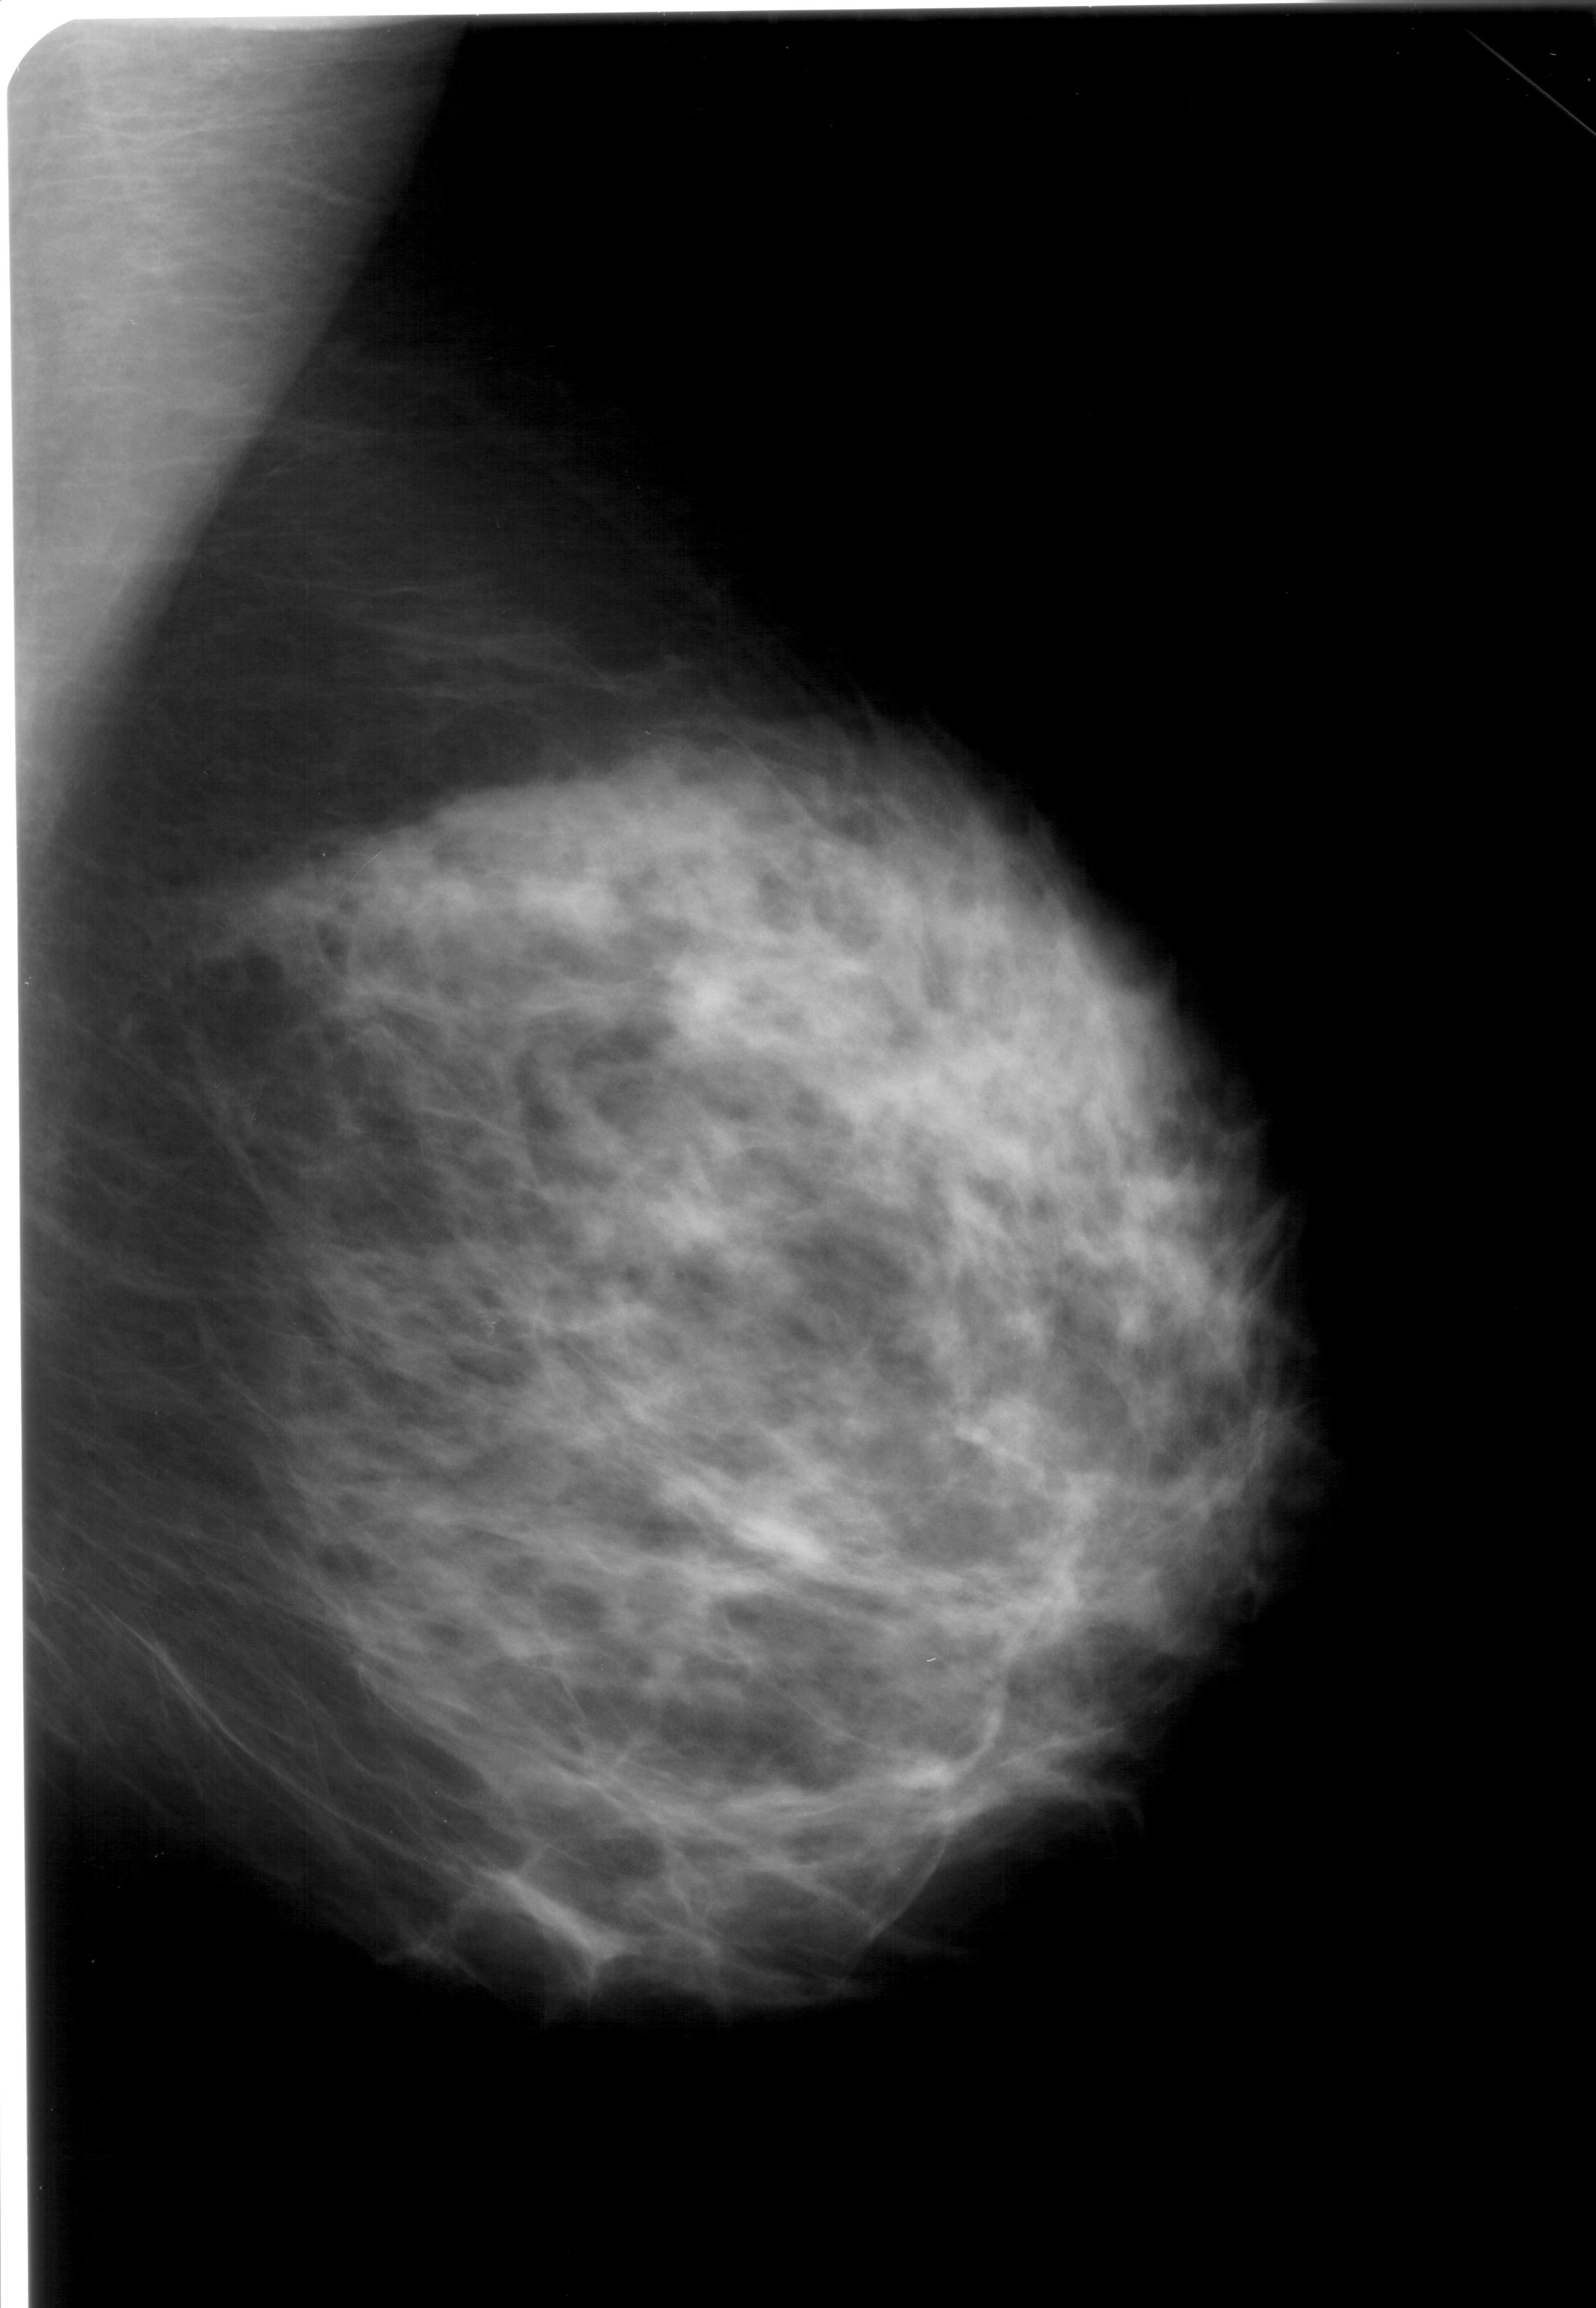
Mammogram (digitized film); right breast; mediolateral oblique (MLO) view; breast composition: heterogeneously dense (BI-RADS density category 3 of 4).
- Radiologist-marked abnormalities on this image: calcifications, morphology pleomorphic, distribution clustered; BI-RADS assessment category 4; pathology result (as recorded, not read from the image): benign.